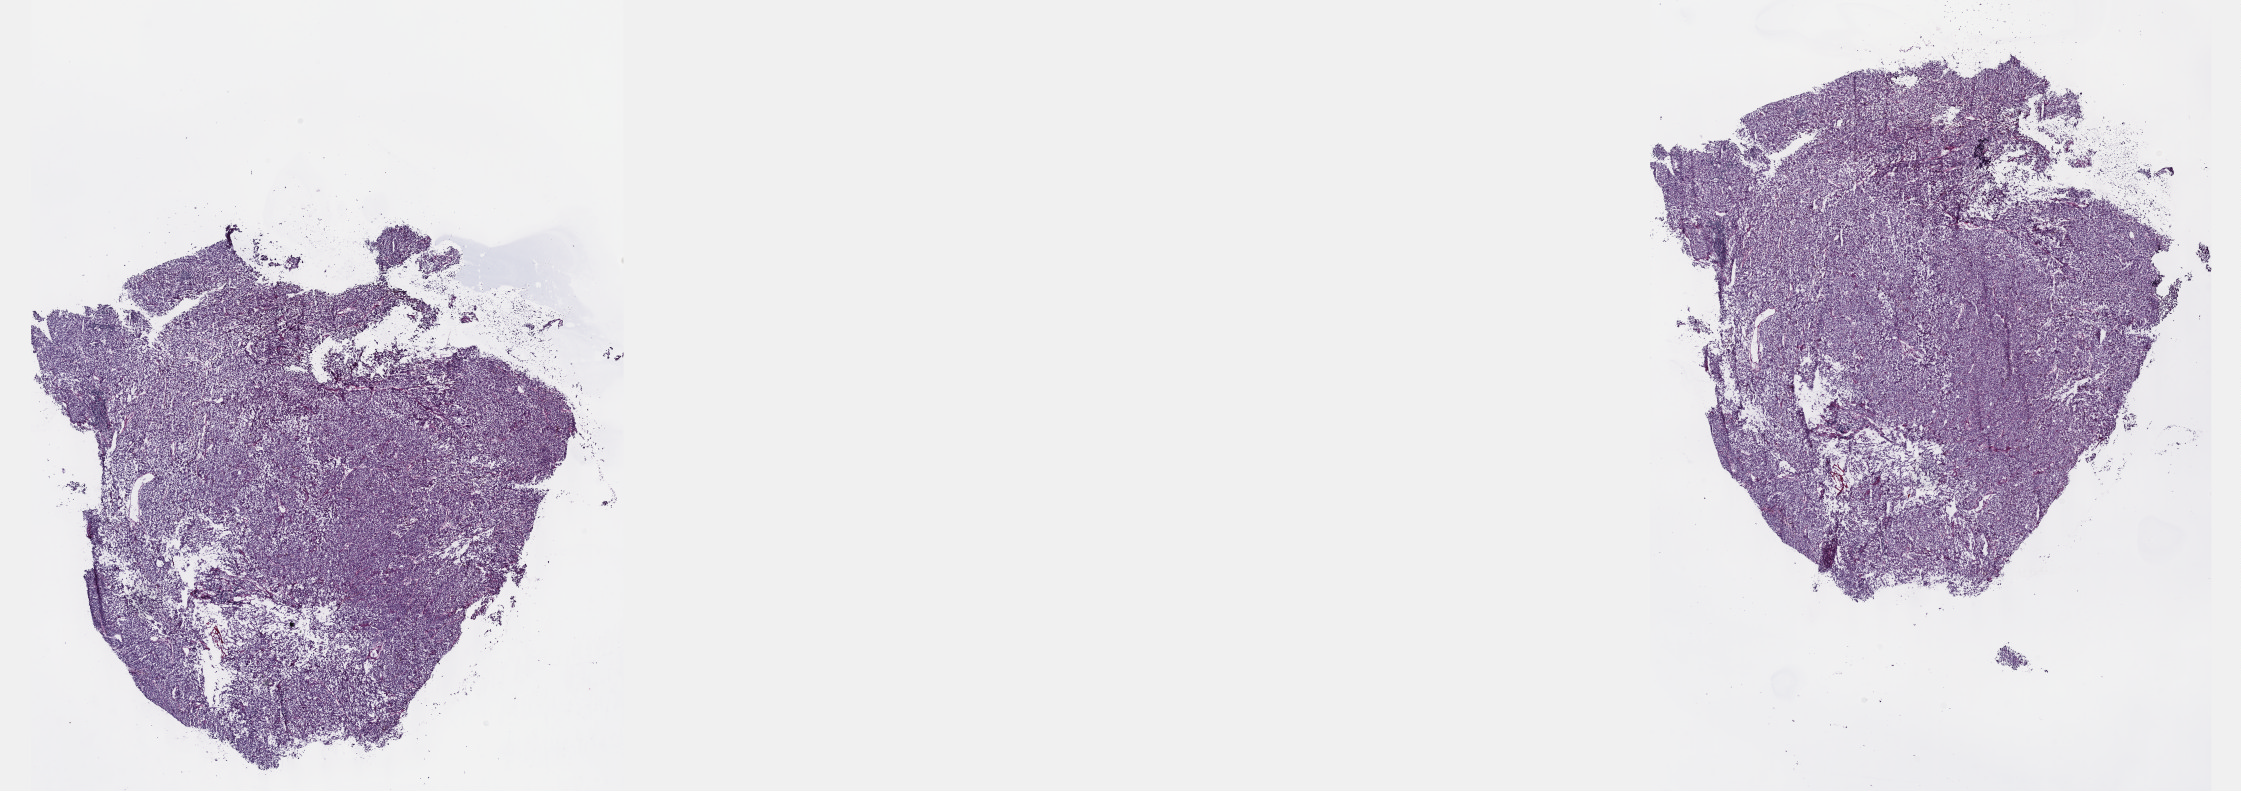
Whole-slide histology image, Hematoxylin and eosin (H&E) stained — a low-resolution overview of the entire scanned area, about 36.2 x 12.8 mm; frozen section; metastatic tumour sample. Patient: male, age at initial diagnosis 68 years. Pathologist review of this section (percent, as recorded): tumour cells 100%, tumour nuclei 80%, normal cells 0%, stromal cells 0%, necrosis 0%. Inflammatory infiltration, as recorded: lymphocyte infiltration 3%, monocyte infiltration 0%, neutrophil infiltration 0%.
This section: metastatic tumour tissue. Patient diagnosis: Malignant melanoma, NOS.